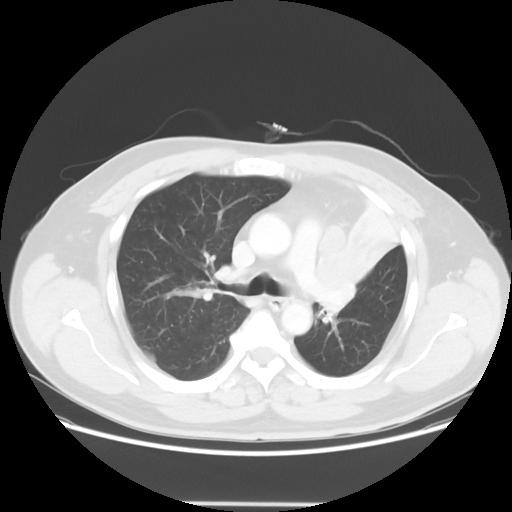
Chest CT, one axial slice; slice 40 of 62 in the series (ordered by position); 120 kVp; lung window (W 1500 / L -600 HU); 5 mm slice thickness; 512 × 512 image matrix. Male patient, age 49 years. Case-level facts recorded for this patient, not image findings: clinical TNM (as recorded): T3 N3 M1c.
Annotated regions visible in this slice (bounding box drawn by a radiologist):
- lung tumour (recorded histology: squamous cell carcinoma): box from (x=304, y=244) to (x=362, y=318) px